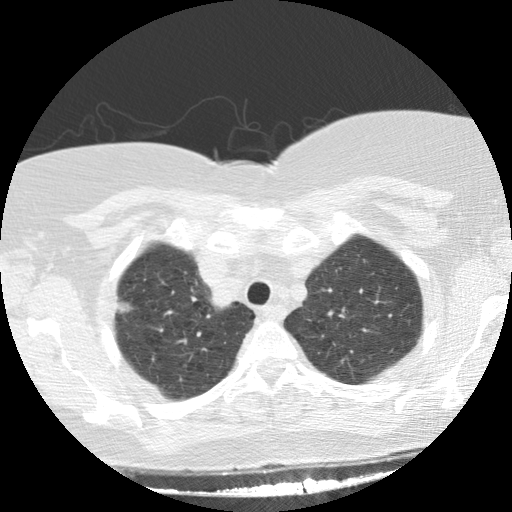
Low-dose screening chest CT, axial slice. Baseline screening round. Lung window (W 1500 / L -600 HU). 120 kVp. 512 × 512 image matrix, field of view 330 × 330 mm. Female, age 64 years at enrolment. Current smoker at enrolment.
Expert-annotated lung lesion, box from (x=100, y=281) to (x=146, y=330) px. Screening reader's record for this exam (one nodule recorded; not confirmed to be the boxed lesion): non-calcified nodule or mass ≥4 mm, right upper lobe, 17 × 16 mm, spiculated (stellate) margins, soft tissue attenuation. Lung cancer was diagnosed 70 days after this screen: adenocarcinoma, NOS, right upper lobe, stage IIIA (AJCC 6th edition), 15 mm at pathology.